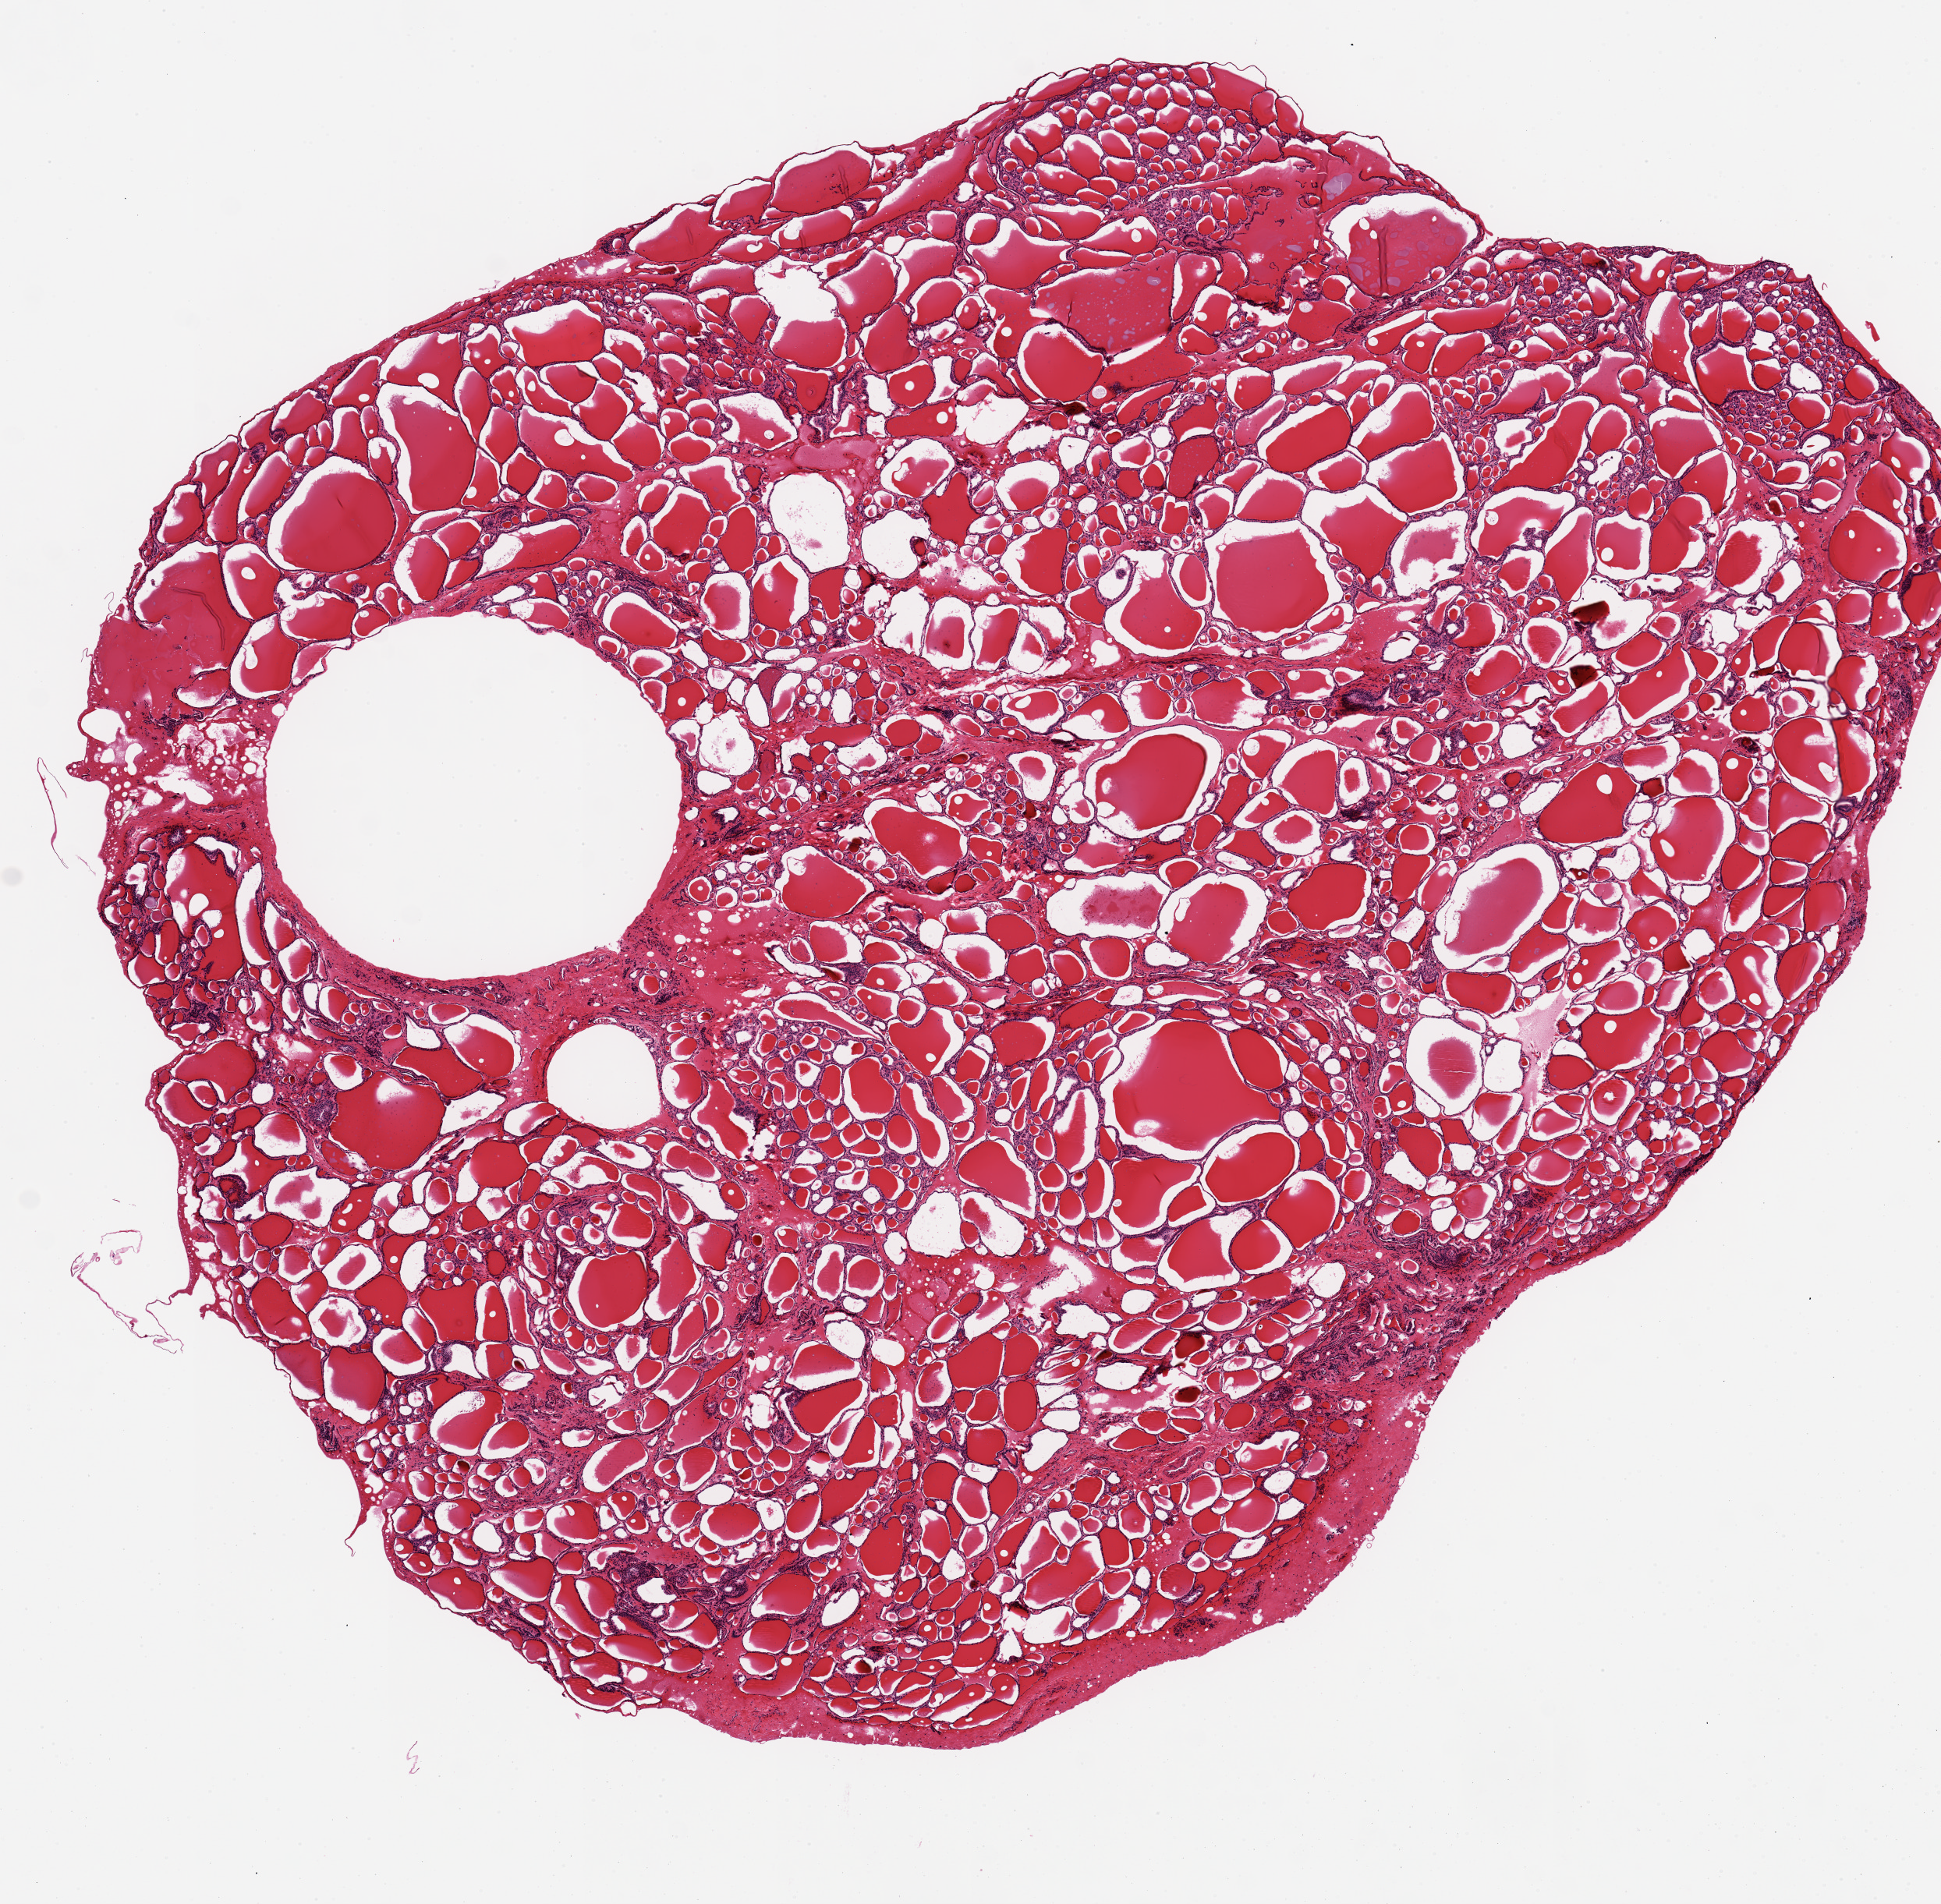
Whole-slide image, haematoxylin and eosin stain, whole scanned area (about 9.8 x 9.7 mm, from a 20x scan) shown as a low-resolution overview. PAXgene-fixed paraffin-embedded (PFPE) section. Target tissue: thyroid. Tissue donor sample. Donor sex: female.
Review note (as recorded): Slight nodularity. 9x8.6mm.